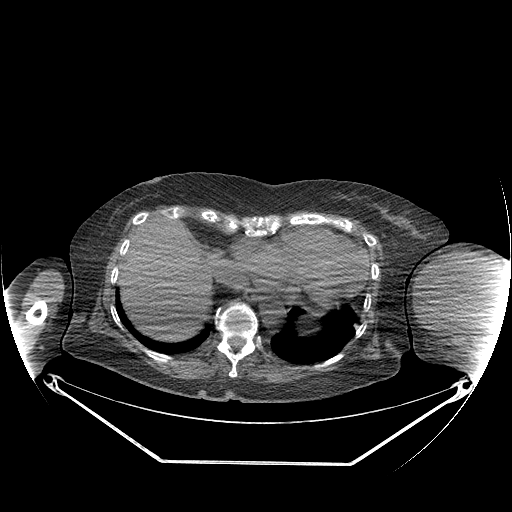
CT of an extremity soft-tissue mass (from a PET/CT study), one axial slice. Position 148 of 267 along the scan axis. 140 kVp. Soft-tissue window (W 400 / L 40 HU). 3.75 mm slice thickness. 512 × 512 image matrix. Female patient. Case-level facts recorded for this patient, not image findings: histological type: pleiomorphic leiomyosarcoma; grade: high; site of the primary tumour: left biceps.
Annotated regions visible in this slice (expert contour drawn on MRI and transferred to this co-registered scan by the dataset authors):
- gross tumour volume including surrounding oedema: bounding box [x1, y1, x2, y2] px = [418, 251, 497, 325]
- gross tumour volume (mass): [418, 251, 497, 323]